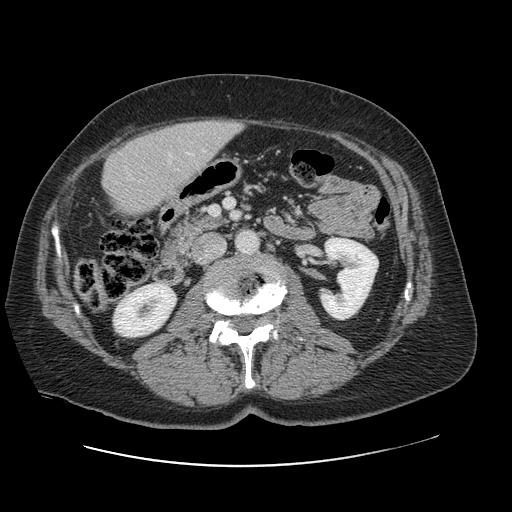
Contrast-enhanced abdominal CT, one axial slice. Position 26 of 138 along the scan axis. 120 kVp. Intravenous contrast given. Soft-tissue window (W 400 / L 40 HU). 512 × 512 image matrix, field of view 402 × 402 mm. Male patient, age 71 years. Case-level facts recorded for this patient, not image findings: diagnosis: colorectal cancer liver metastases, imaged before liver resection; multiple liver metastases: no; largest metastasis: 3.3 cm; chemotherapy before resection: no.
Outlined on this slice (manually delineated by an expert):
- liver: bounding box (x1, y1, x2, y2) in pixels: (103, 120, 241, 216)
- planned liver remnant (the part of the liver to remain after resection): (102, 134, 179, 215)